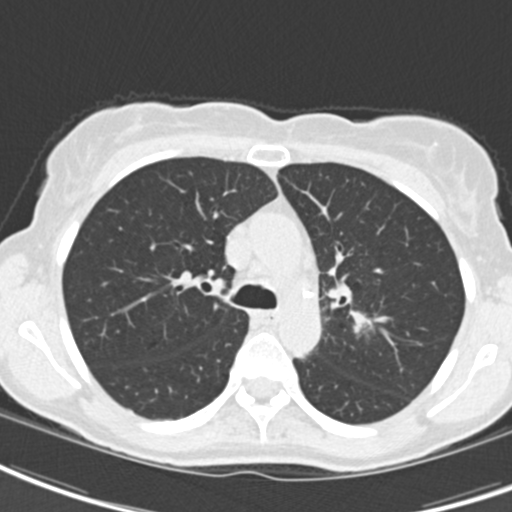
Low-dose screening chest CT, axial slice. Baseline annual screen. Lung window (W 1500 / L -600 HU). Standard (soft-tissue) reconstruction kernel (B30f). 512 × 512 image matrix, field of view 279 × 279 mm. Female participant, aged 62 years at enrolment. Current smoker at enrolment.
- Expert reader's lesion annotation, bounding box [x1, y1, x2, y2] px = [291, 254, 364, 340].
- Screening reader's record for this exam (one nodule recorded; not confirmed to be the boxed lesion): non-calcified nodule or mass ≥4 mm, right upper lobe, 24 × 20 mm, smooth margins, ground glass attenuation.
- Note: the box lies in the patient's left hemithorax on this image, whereas the reader's record names the right lung; they may be different findings.